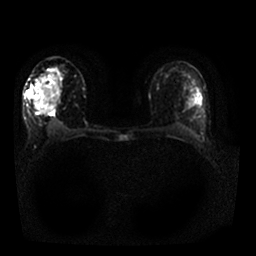
Breast MRI, one axial slice. Position 9 of 25 along the scan axis. Diffusion-weighted series; image 2 of 4 stored at this slice position (different b-values; order by instance number). 1.5 T. 4 mm slice thickness. 256 × 256 image matrix. Female patient.
Annotated regions visible in this slice (expert manual segmentation):
- tumour on diffusion-weighted imaging: bounding box (x1, y1, x2, y2) in pixels: (27, 89, 33, 97)